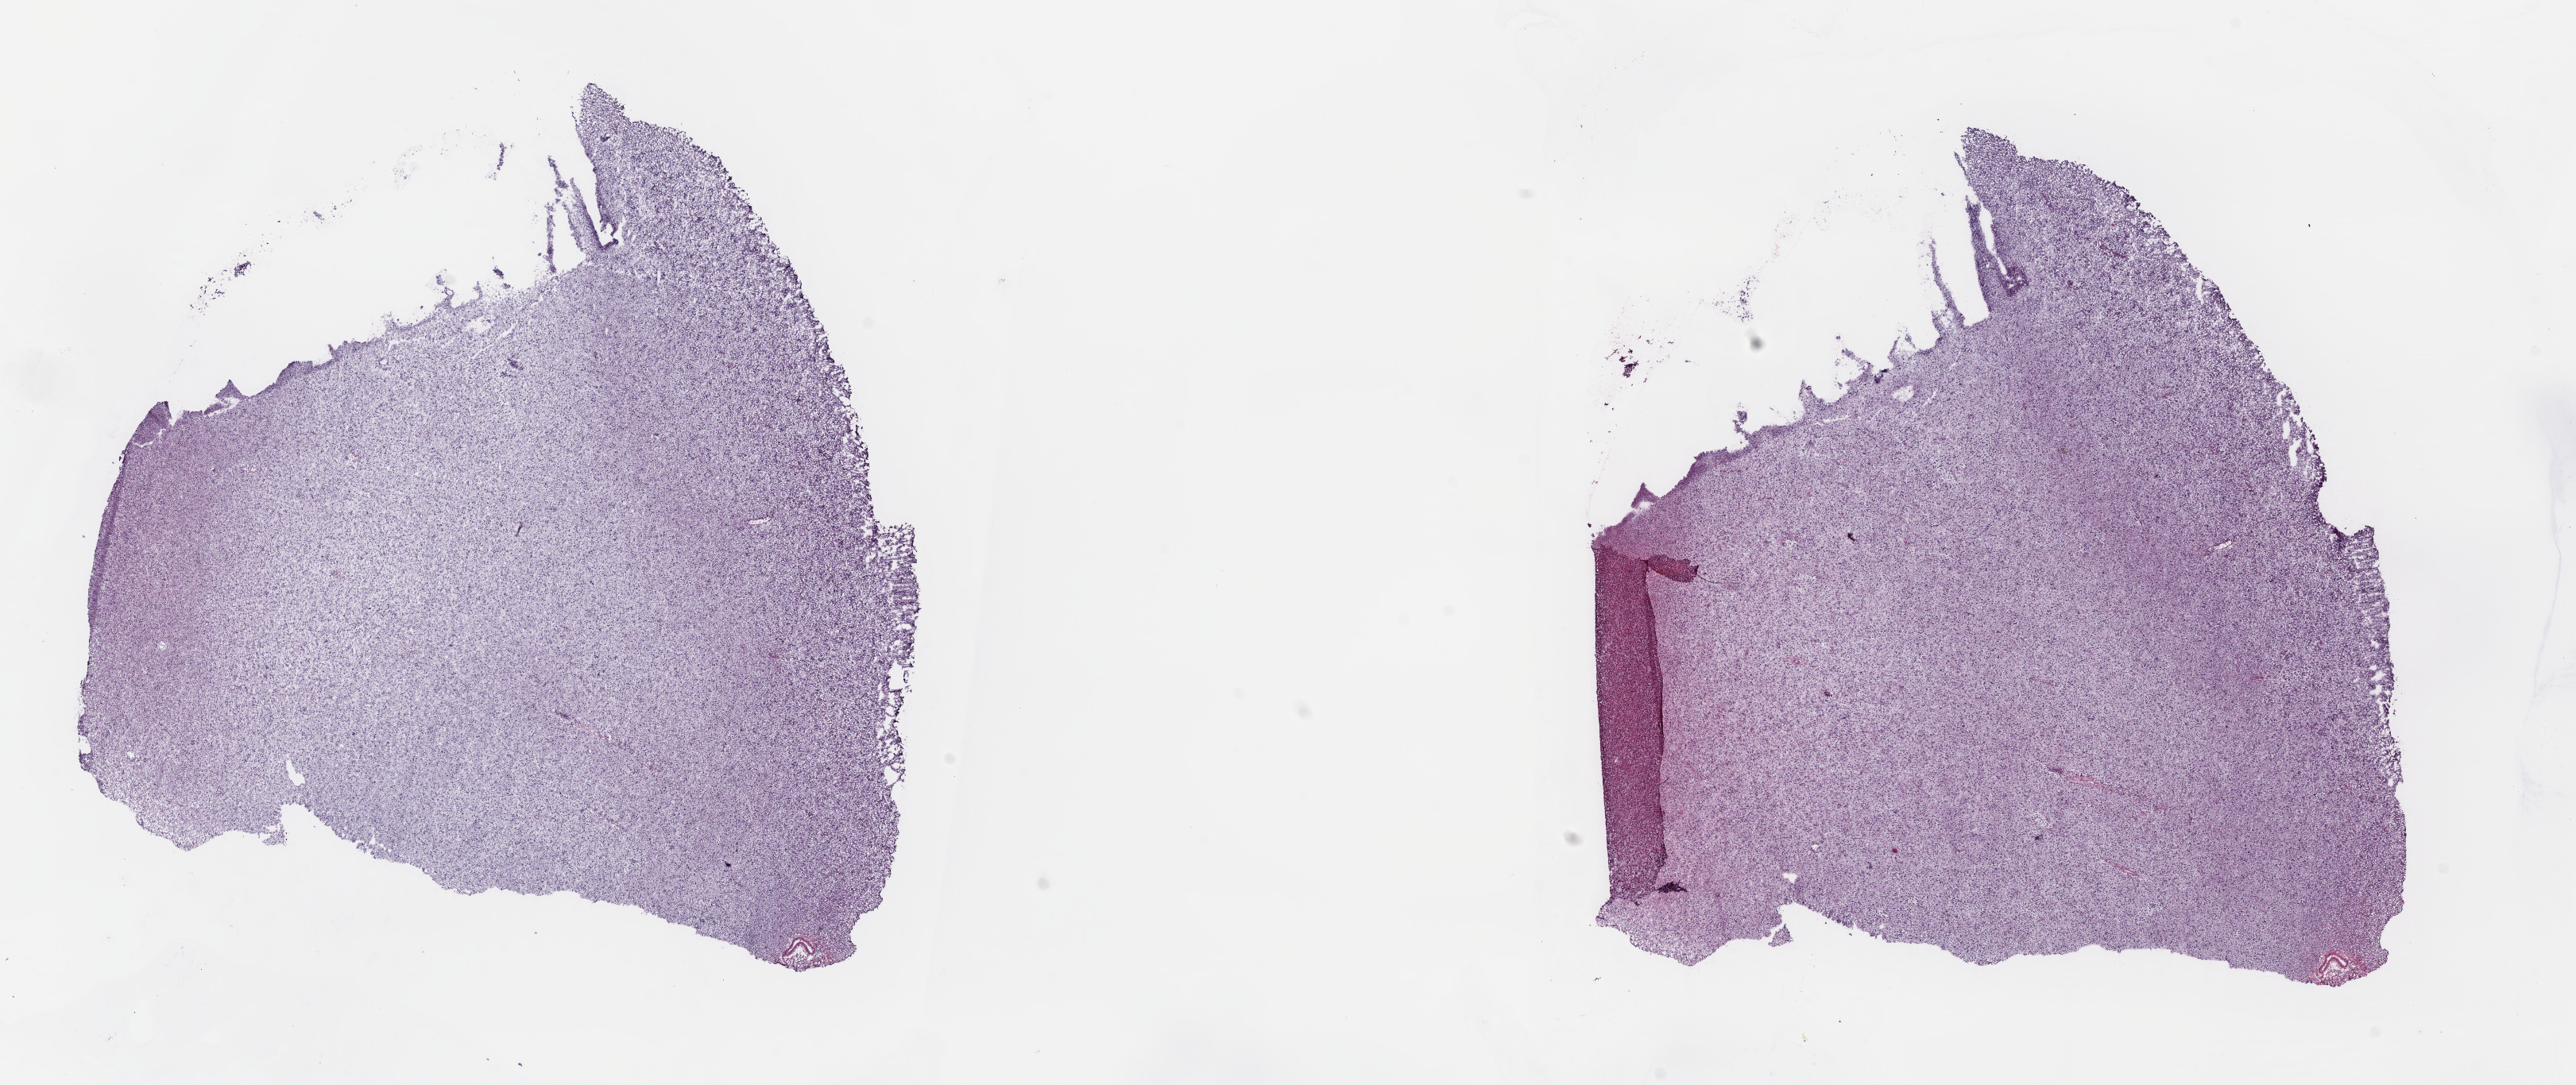
Digitized H&E tissue section (whole slide), shown as a low-resolution overview of the whole scanned area (about 25.5 x 10.7 mm, slide scanned at 40x), frozen section, sample: primary tumour, brain. Male patient; age at initial diagnosis 38 years. Histologic grade: G3 (poorly differentiated). Composition of this section per pathologist review: tumour cells 90%, tumour nuclei 90%, normal cells 10%, stromal cells 0%, necrosis 0%. Inflammatory infiltration, as recorded: lymphocyte infiltration 0%, monocyte infiltration 0%, neutrophil infiltration 0%.
* laterality: left
* diagnosis: Astrocytoma, anaplastic (occipital lobe)